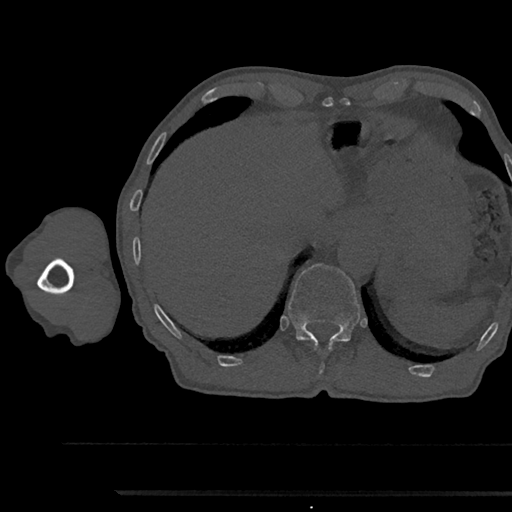
CT including the spine, one axial slice; position 743 of 797 along the scan axis; reconstruction kernel Br40s/3; 120 kVp; bone window (W 1800 / L 400 HU); 0.5 mm slice thickness; 512 × 512 image matrix. Male patient, age 79 years. Case-level facts recorded for this patient, not image findings: primary cancer: prostate.
Structures marked on this image (semi-automatically segmented with operator editing):
- T11 vertebra: bounding box <329,344,332,350> (left, top, right, bottom; pixels)
- T12 vertebra: <288,264,360,346>